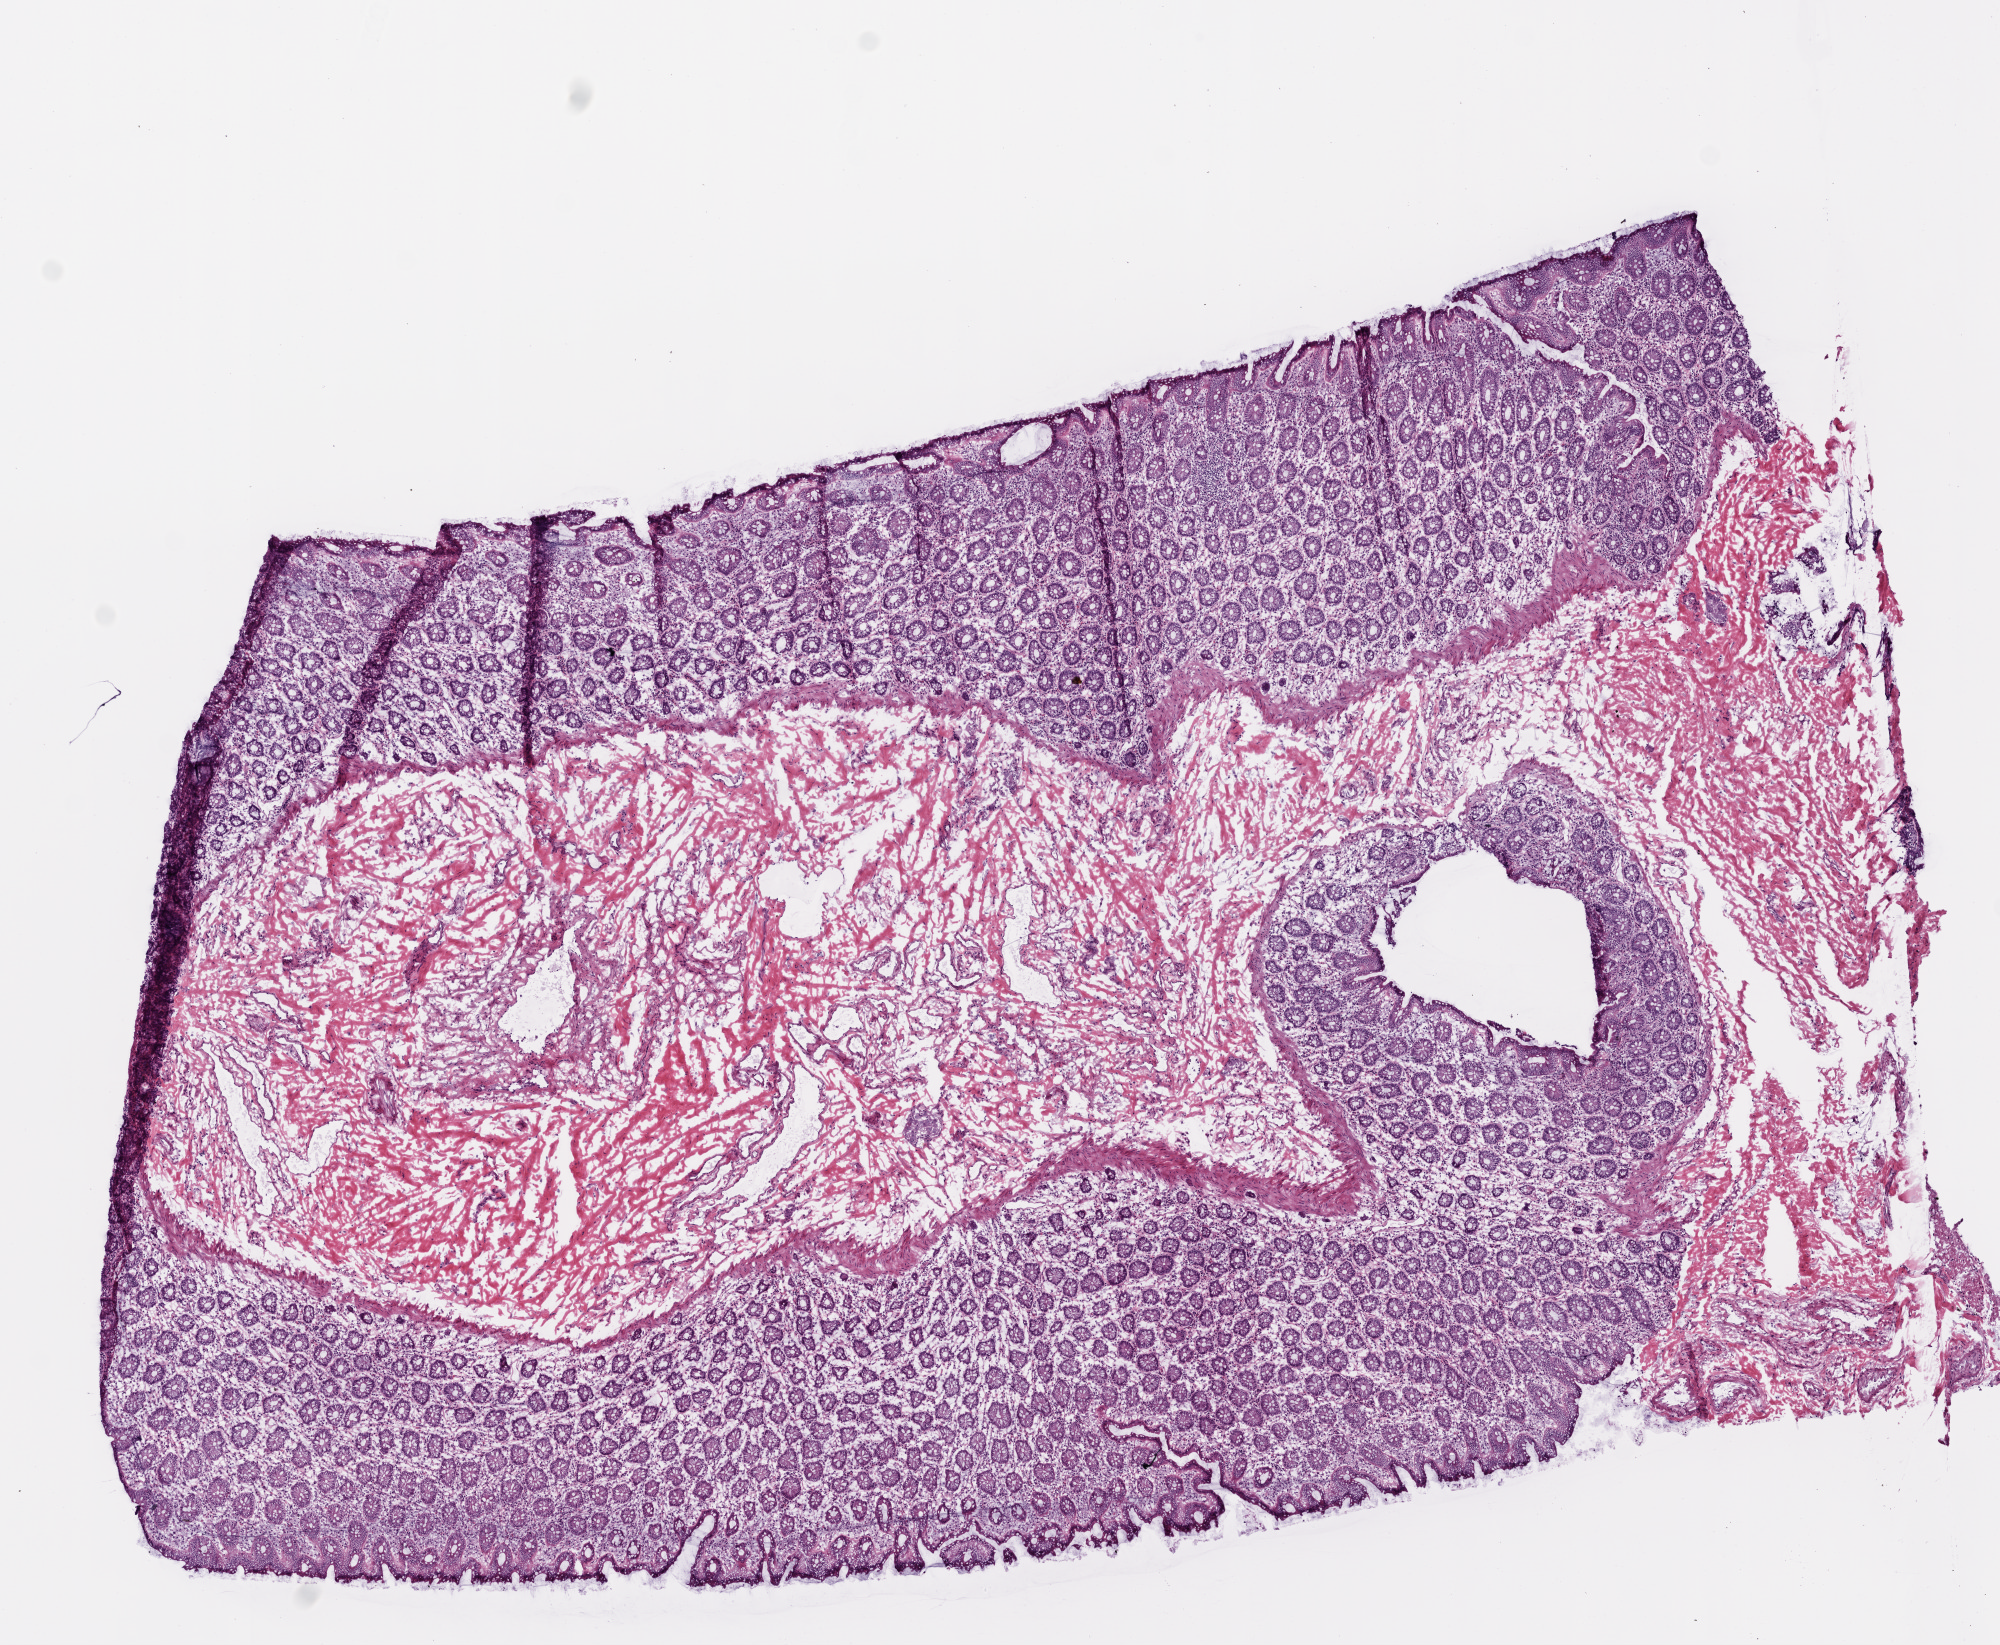
Digitized H&E tissue section (whole slide) — shown as a low-resolution overview of the whole scanned area (about 8.0 x 6.6 mm); frozen section from the top of the tissue portion; solid tissue normal (non-tumour tissue) sample from the colon. Female patient; age at initial diagnosis 81 years.
This section: solid tissue normal (non-tumour) sample from the same patient. Patient diagnosis: Adenocarcinoma, NOS (cecum).